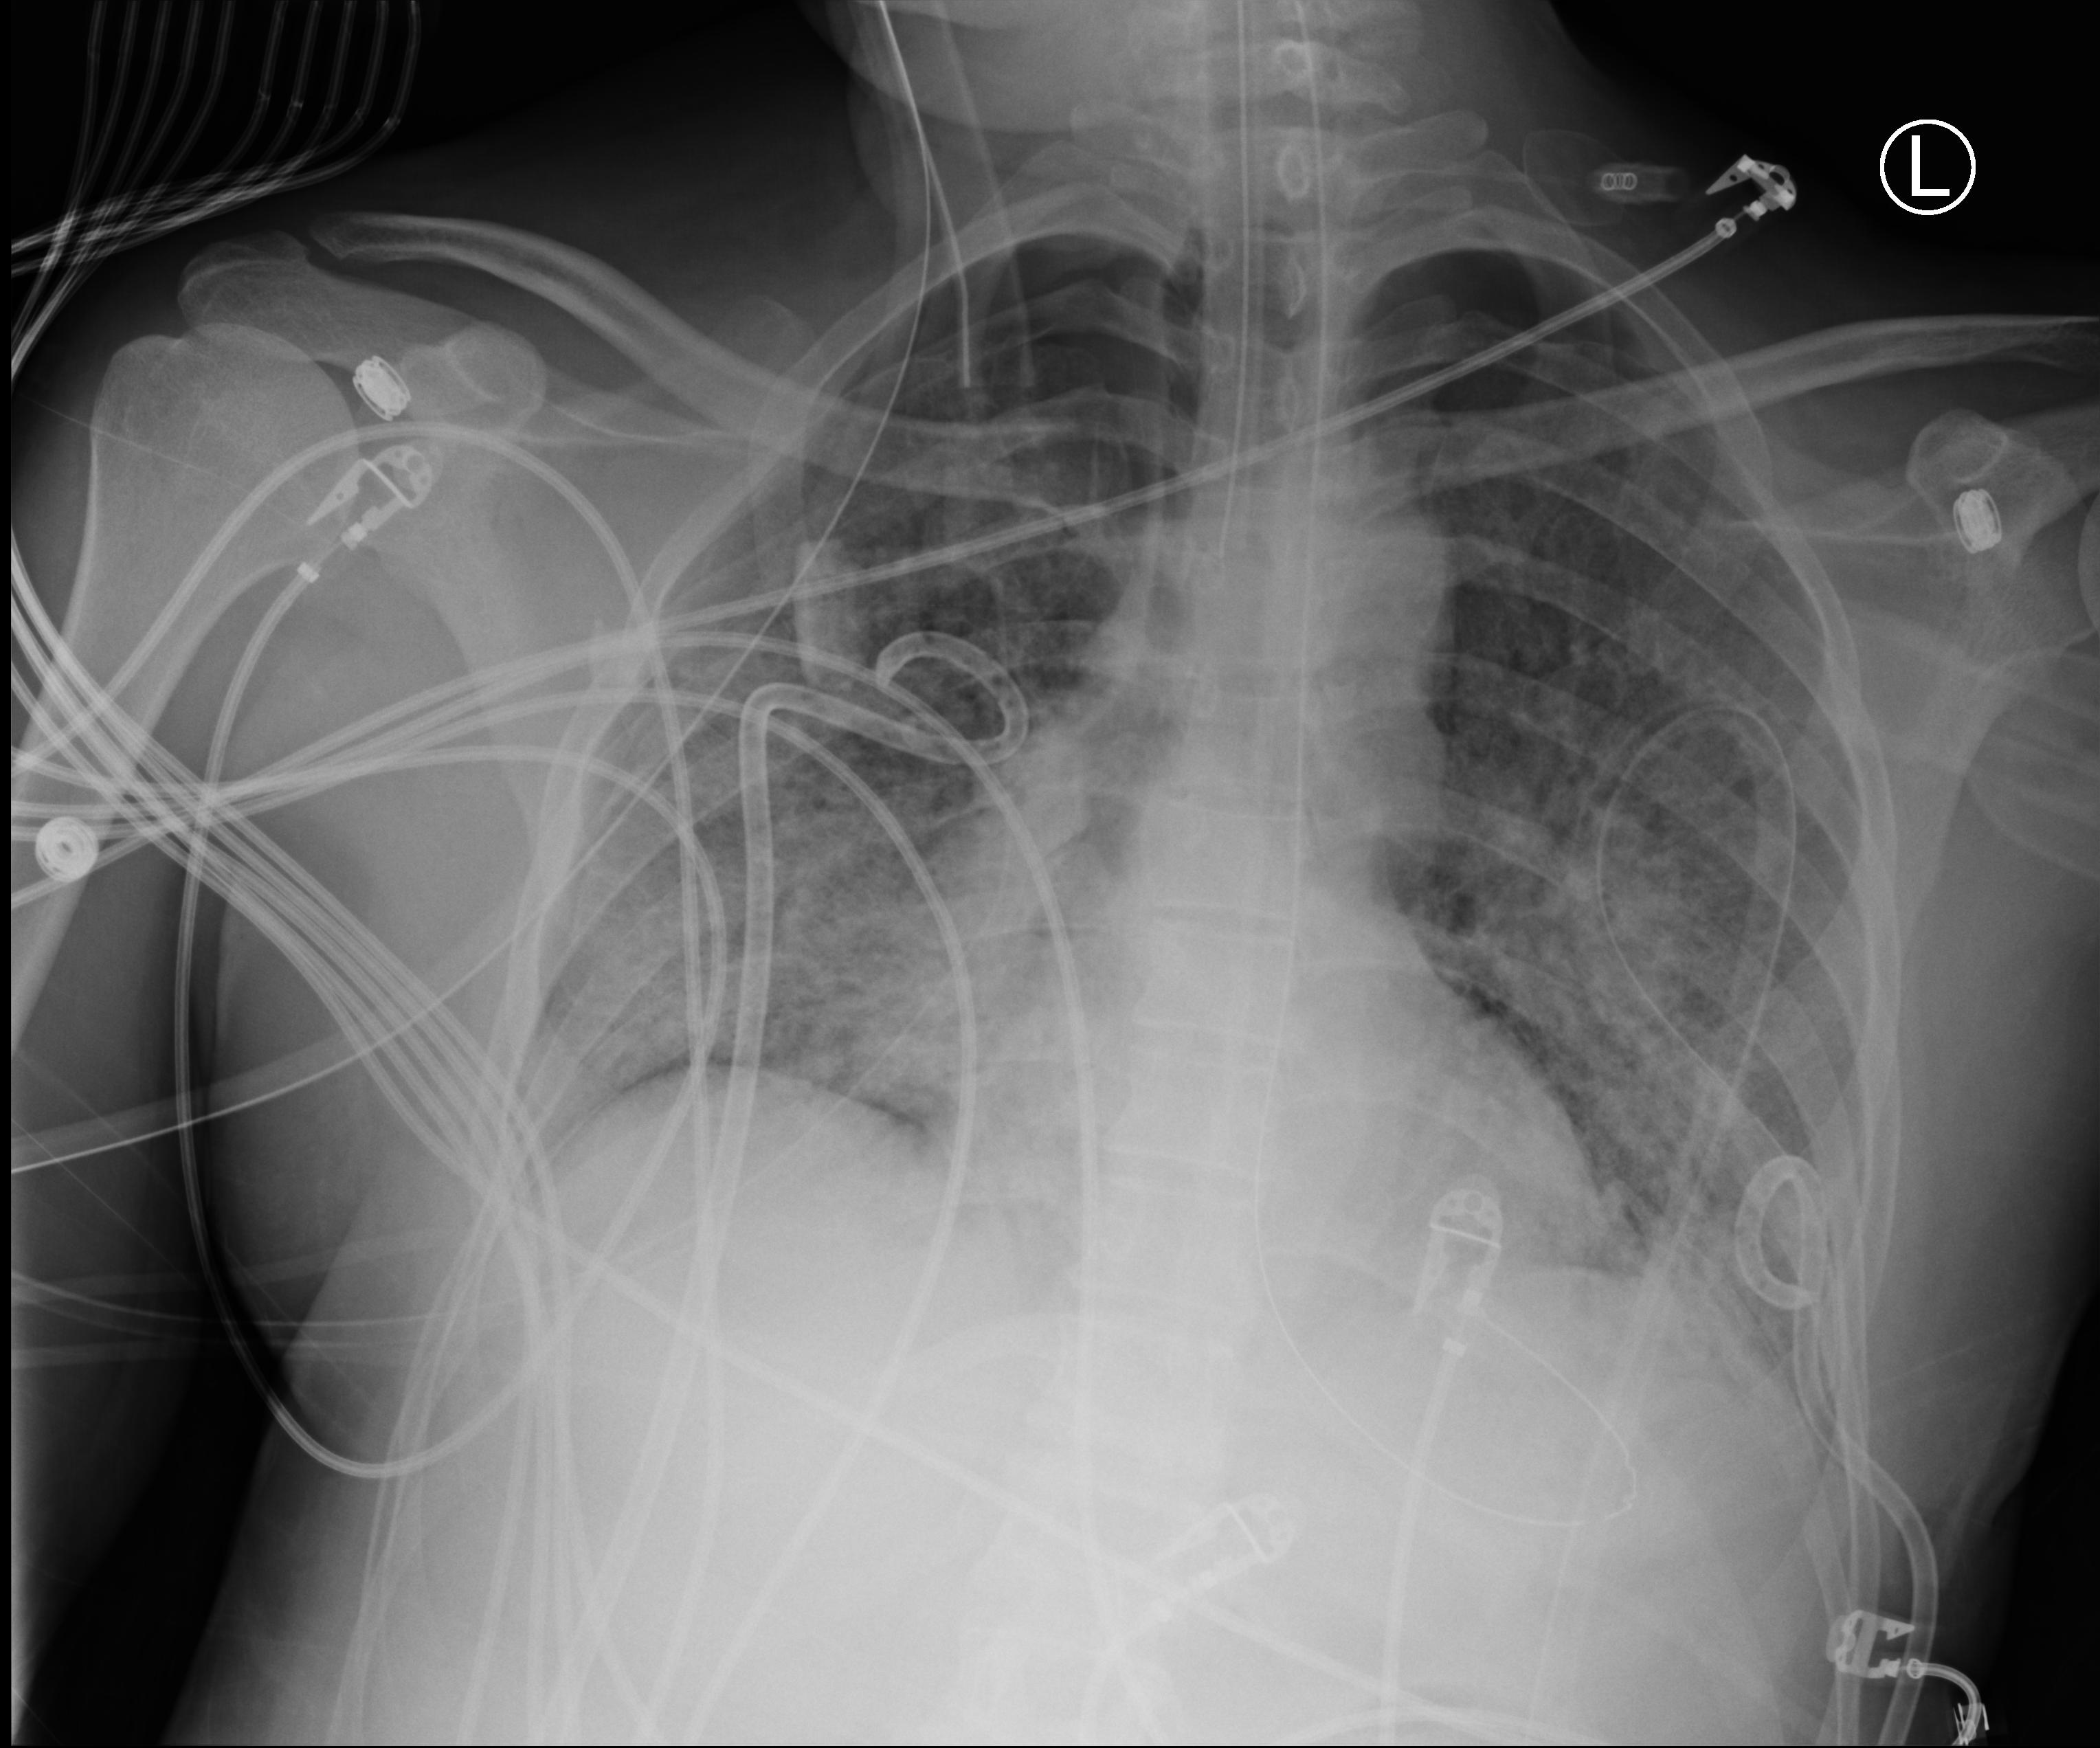
Bedside chest radiograph (computed radiography), anteroposterior (AP) projection. Patient hospitalised with COVID-19, aged 18–59 years.
Hospital-stay facts (about this admission, not read from this image; timing relative to this image not recorded):
- mechanically ventilated during this hospital stay: yes
- admitted to intensive care during this hospital stay: yes